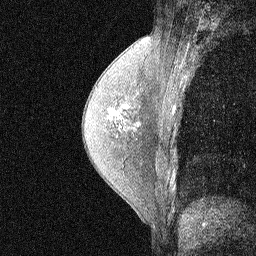
Breast MRI (dynamic contrast-enhanced), one sagittal slice. Slice 35 of 58 in the series (ordered by position). Dynamic contrast-enhanced study with each time point stored as its own series, time point 2 of 3 at this slice position (early post-contrast, ordered by acquisition time). 1.5 T. TE 4.5 ms, TR 11 ms. 2.07 mm slice thickness. 256 × 256 image matrix, field of view 200 × 200 mm. Patient: female, 54 years. From the clinical record (not read from this slice): setting: breast cancer imaged before/during neoadjuvant chemotherapy; receptor status: HR-positive, HER2-negative.
Annotated regions visible in this slice (semi-automatically segmented with operator editing):
- analysis volume of interest (the breast-tissue region the enhancement analysis was run in; not a lesion): bounding box (x1, y1, x2, y2) in pixels: (92, 89, 149, 186)
- tumour enhancement mask (voxels above the 90 % enhancement threshold inside the analysis volume of interest): (111, 110, 118, 116)